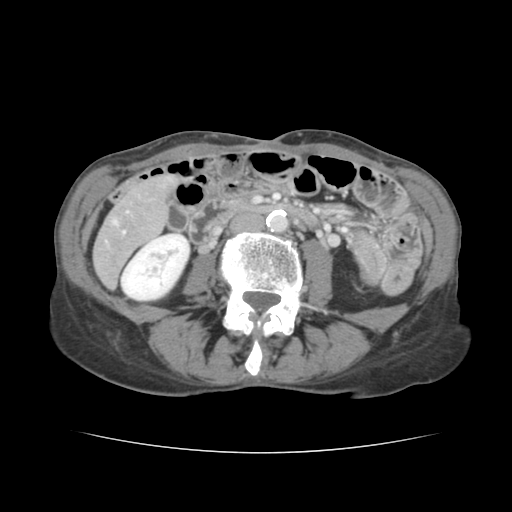
Contrast-enhanced abdominal CT, one axial slice; position 31 of 136 along the scan axis; intravenous contrast given; soft-tissue window (W 400 / L 40 HU); 2.5 mm slice thickness; 512 × 512 image matrix. Female patient, age 77 years. From the clinical record (not read from this slice): diagnosis: colorectal cancer liver metastases, imaged before liver resection; multiple liver metastases: yes; largest metastasis: 3 cm; disease in both lobes: no.
Structures marked on this image (expert manual segmentation):
- liver: box from (x=94, y=177) to (x=174, y=285) px
- portal vein (with intrahepatic branches): (x=123, y=231)–(x=125, y=233)